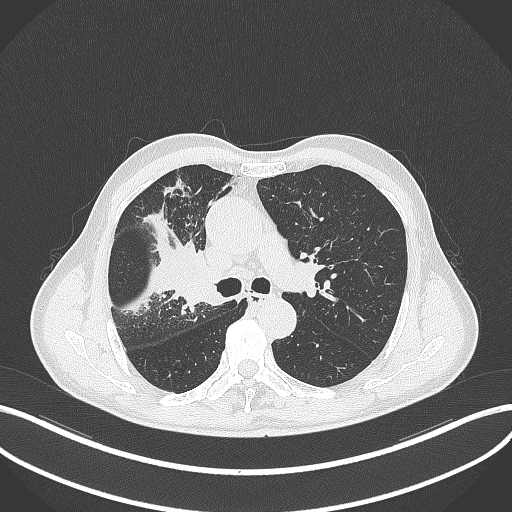
Chest CT, one axial slice; position 315 of 490 along the scan axis; 120 kVp; lung window (W 1500 / L -600 HU); 1 mm slice thickness; 512 × 512 image matrix. Patient: male, 69 years. From the clinical record (not read from this slice): clinical TNM (as recorded): T2a N0 M0.
Outlined on this slice (bounding box drawn by a radiologist):
- lung tumour (recorded histology: adenocarcinoma): bounding box <165,243,226,313> (left, top, right, bottom; pixels)